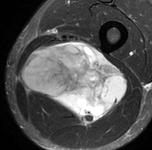
MRI of an extremity soft-tissue mass, one axial slice. Position 48 of 90 along the scan axis. STIR. MR volume resampled by the dataset authors to the PET/CT grid (not the native acquisition matrix). 152 × 150 image matrix, field of view 148 × 146 mm. Male patient. Case-level facts recorded for this patient, not image findings: histological type: undifferentiated pleomorphic liposarcoma; grade: high; site of the primary tumour: left thigh.
Outlined on this slice (expert contour drawn on MRI and transferred to this co-registered scan by the dataset authors):
- gross tumour volume including surrounding oedema: bounding box <23,43,129,127> (left, top, right, bottom; pixels)
- gross tumour volume (mass): <25,43,129,127>